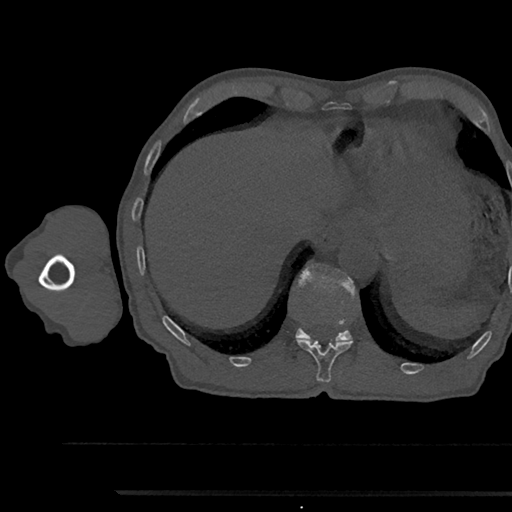
CT including the spine, one axial slice; slice 757 of 797 in the series (ordered by position); bone window (W 1800 / L 400 HU); 512 × 512 image matrix, field of view 367 × 367 mm. Male patient, age 79 years. From the clinical record (not read from this slice): primary cancer: prostate.
Outlined on this slice (semi-automatically segmented with operator editing):
- T11 vertebra: bounding box (x1, y1, x2, y2) in pixels: (297, 338, 352, 382)
- T12 vertebra: (295, 264, 357, 342)